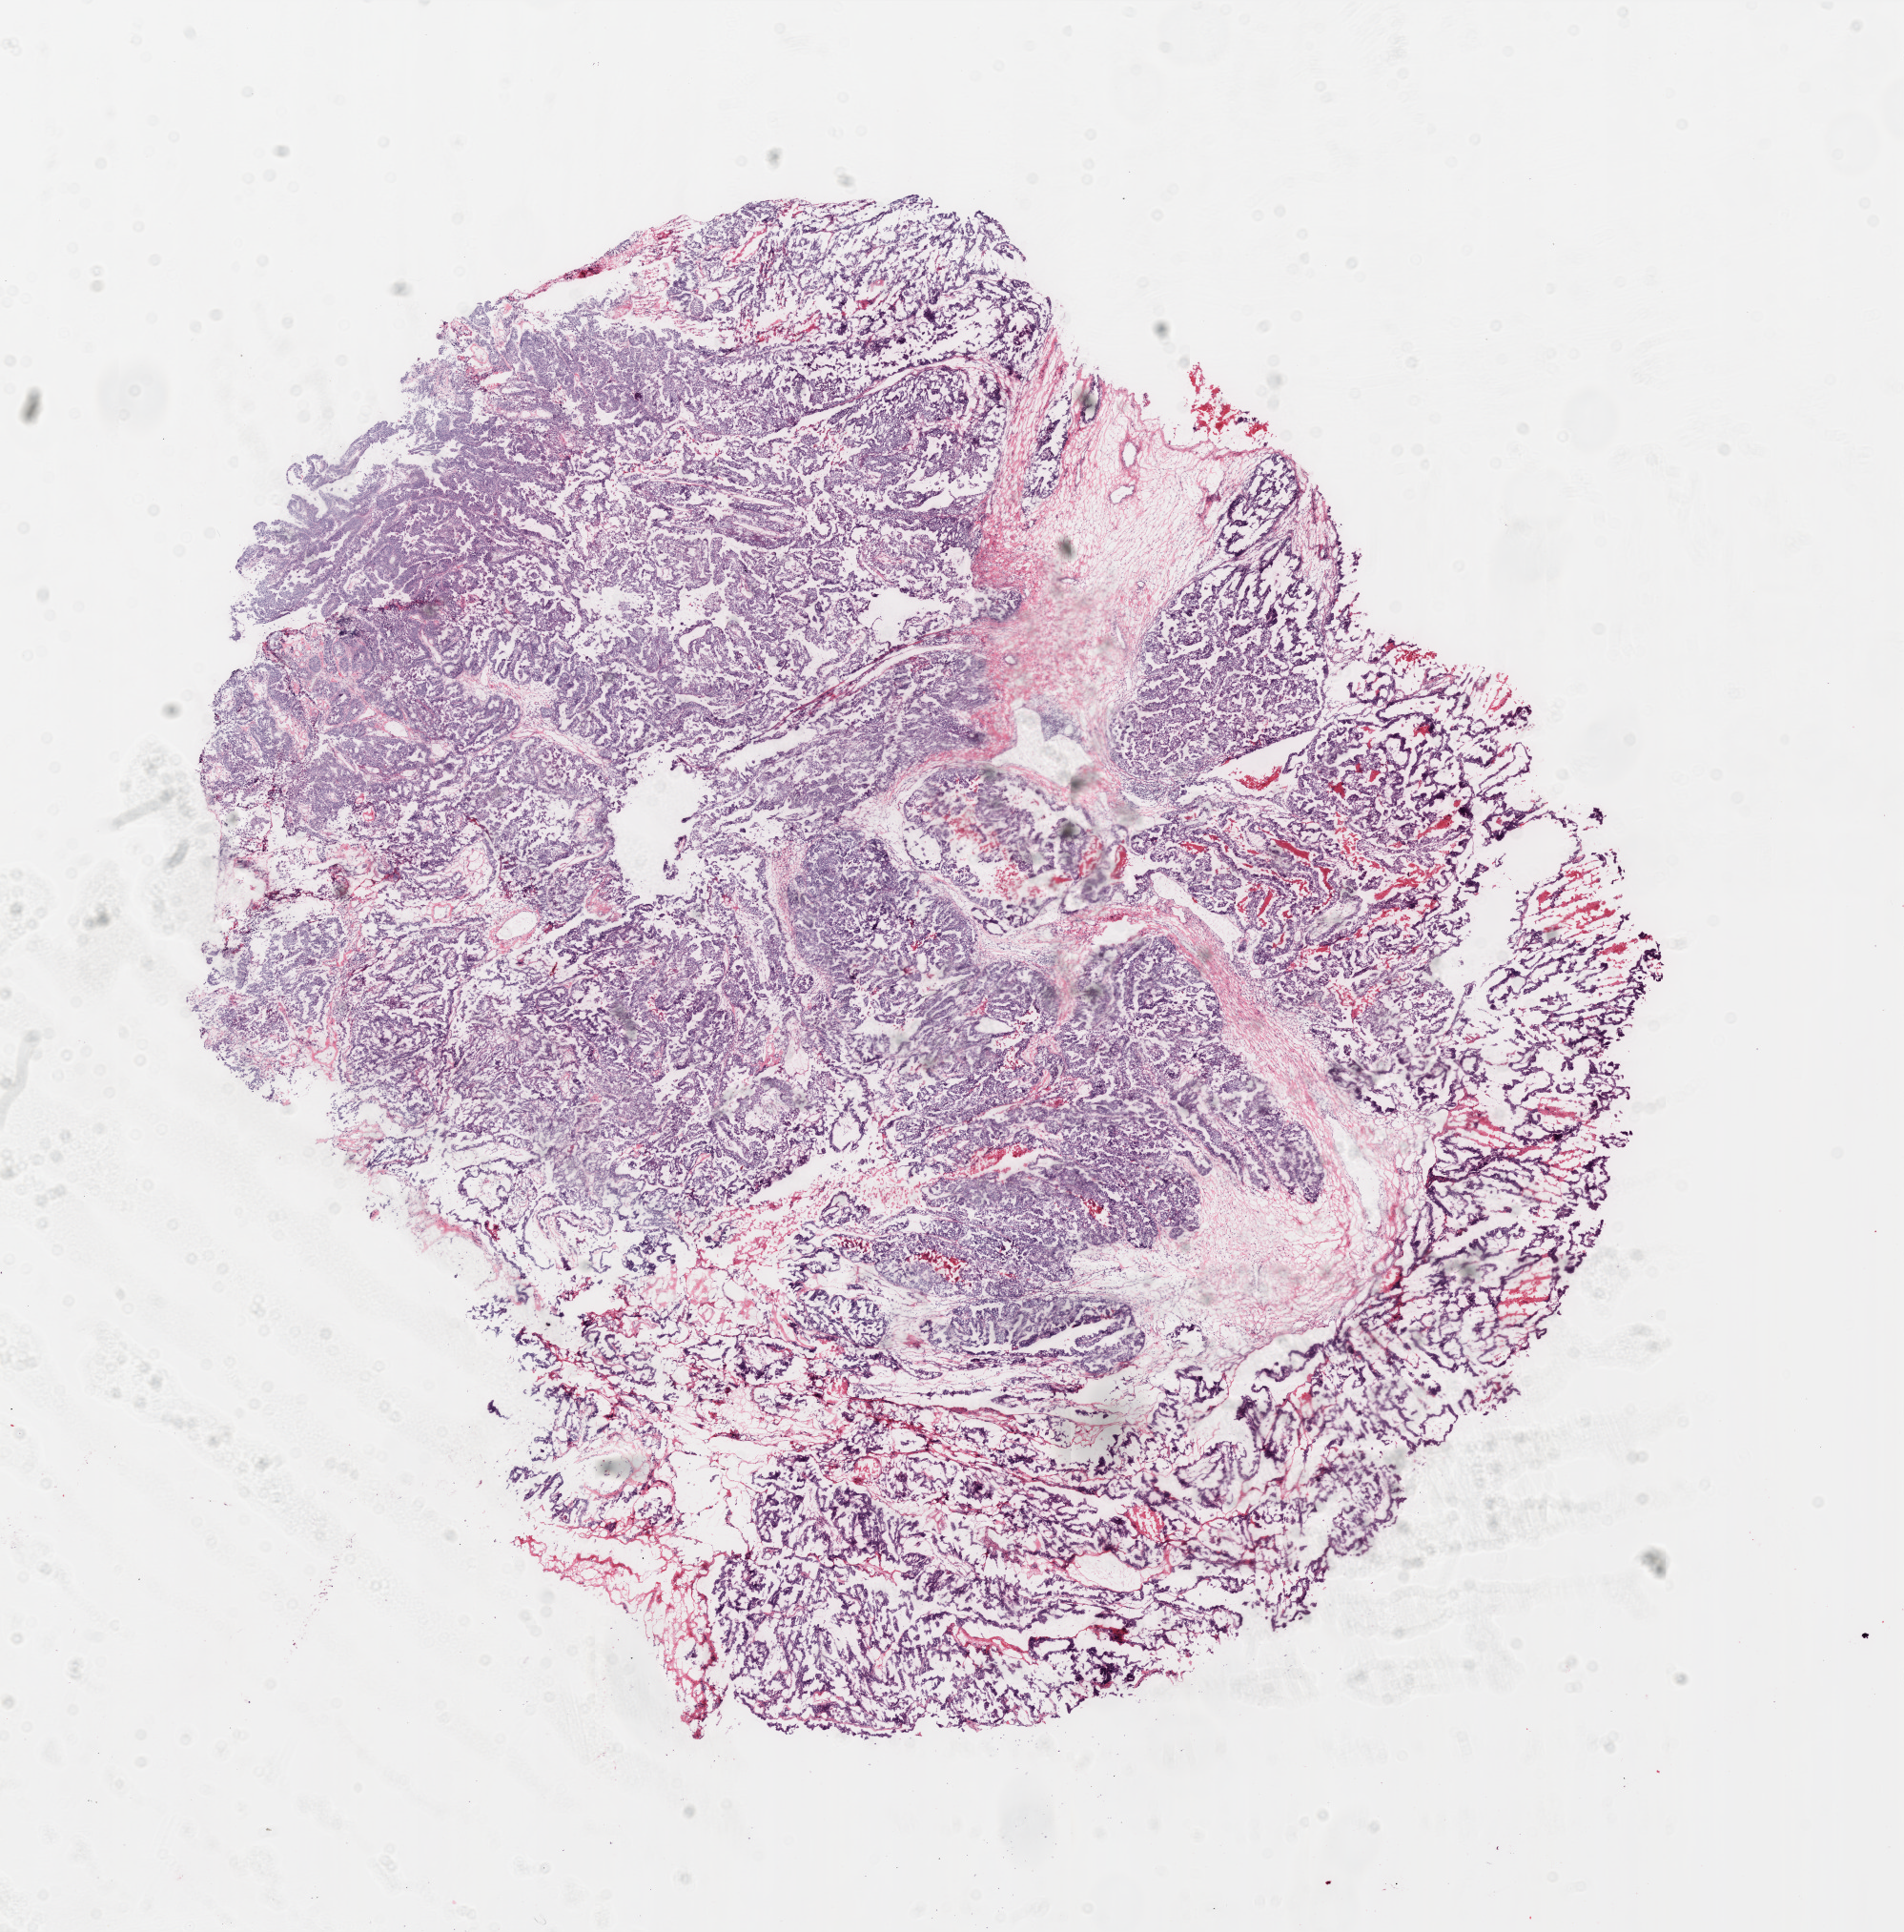
Digitized H&E tissue section (whole slide), a low-resolution overview of the entire scanned area, about 16.0 x 16.2 mm, frozen section from the top of the tissue portion, primary tumour sample from the ovary. Patient: female, age at initial diagnosis 74 years. Pathologist review of this section (percent, as recorded): tumour cells 85%, tumour nuclei 90%.
Diagnosis: Serous cystadenocarcinoma, NOS.